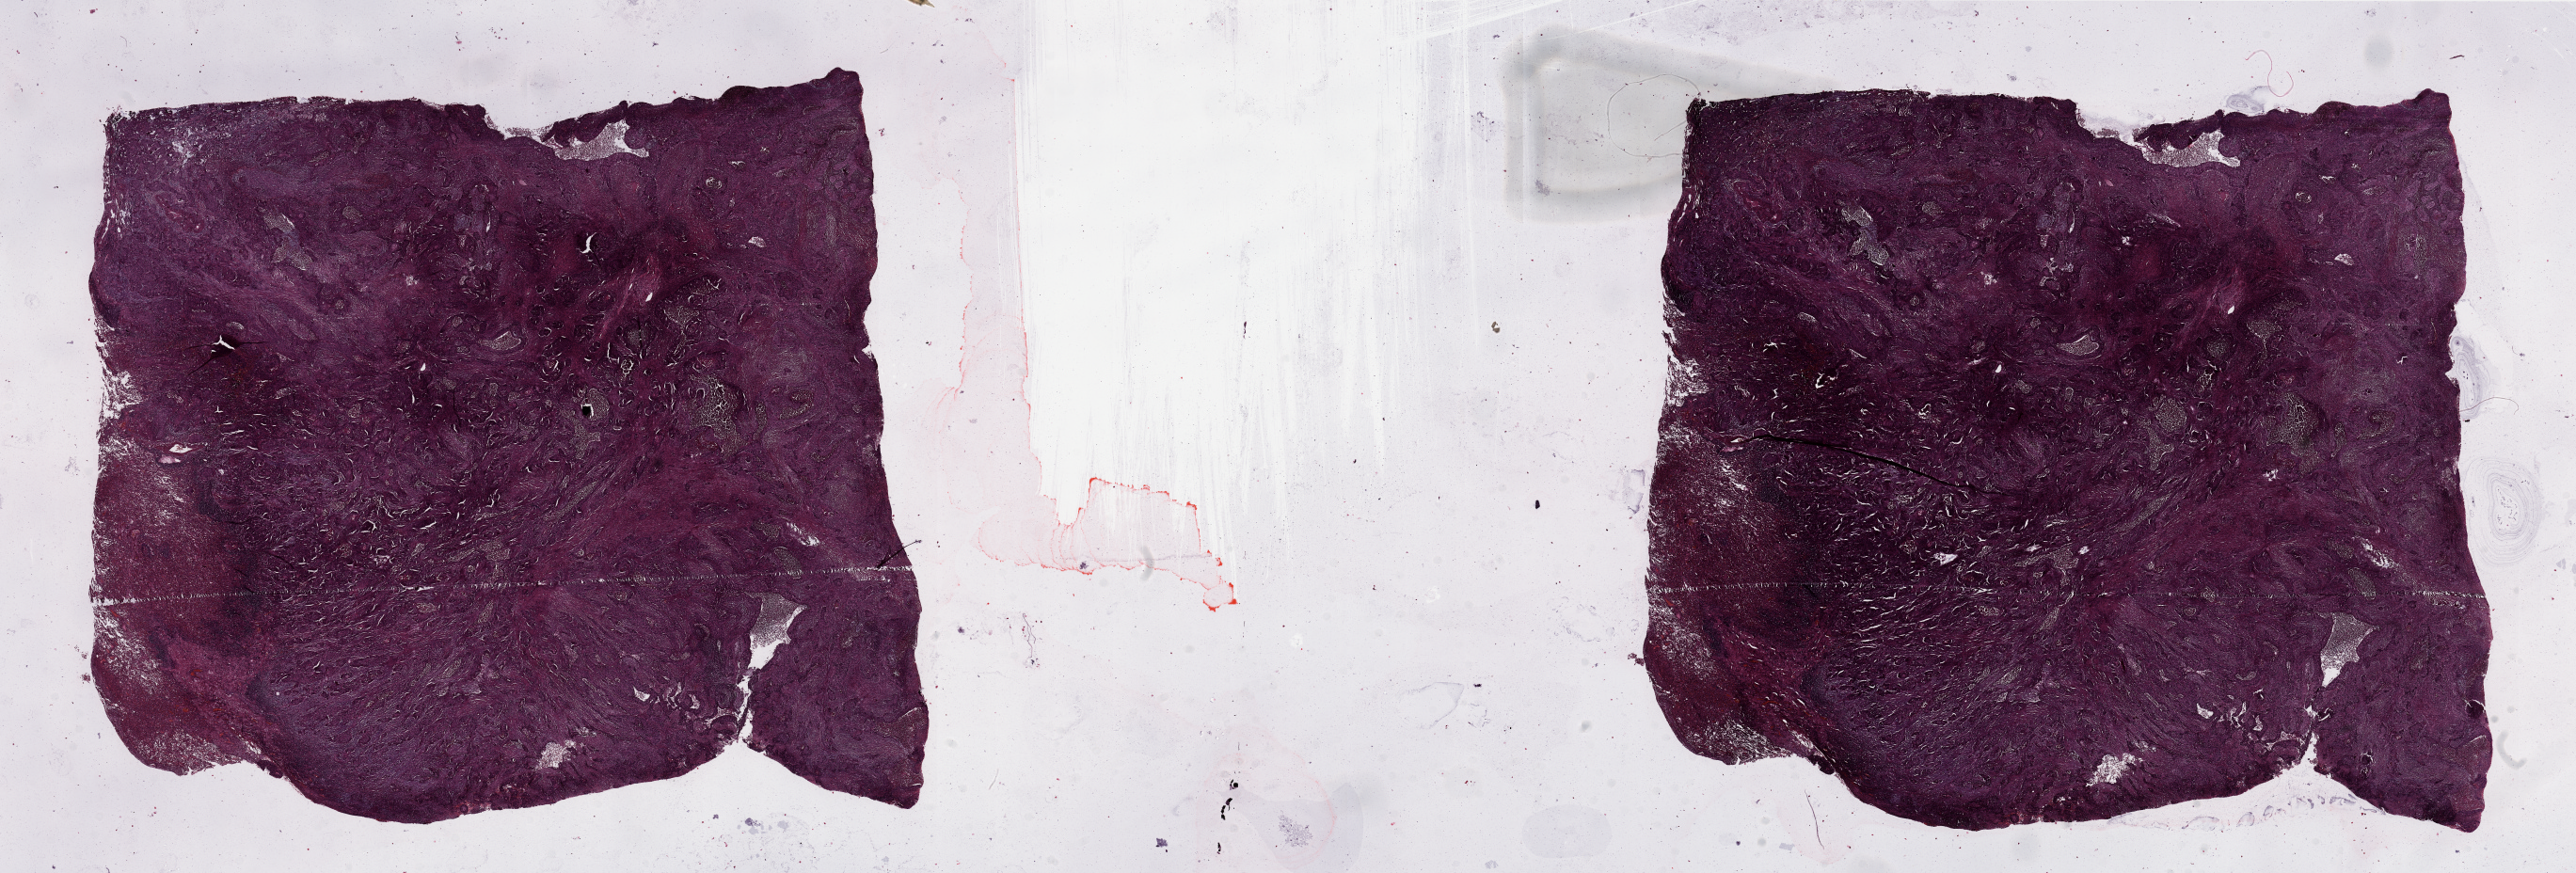
Digitized H&E tissue section (whole slide) — shown as a low-resolution overview of the whole scanned area (about 43.3 x 14.7 mm, slide scanned at 20x); tumour tissue sample, lung. Patient: male, age 66 years. Histologic grade: G1 (well differentiated).
* histologic diagnosis: Squamous cell carcinoma, NOS
* AJCC pathologic stage: II